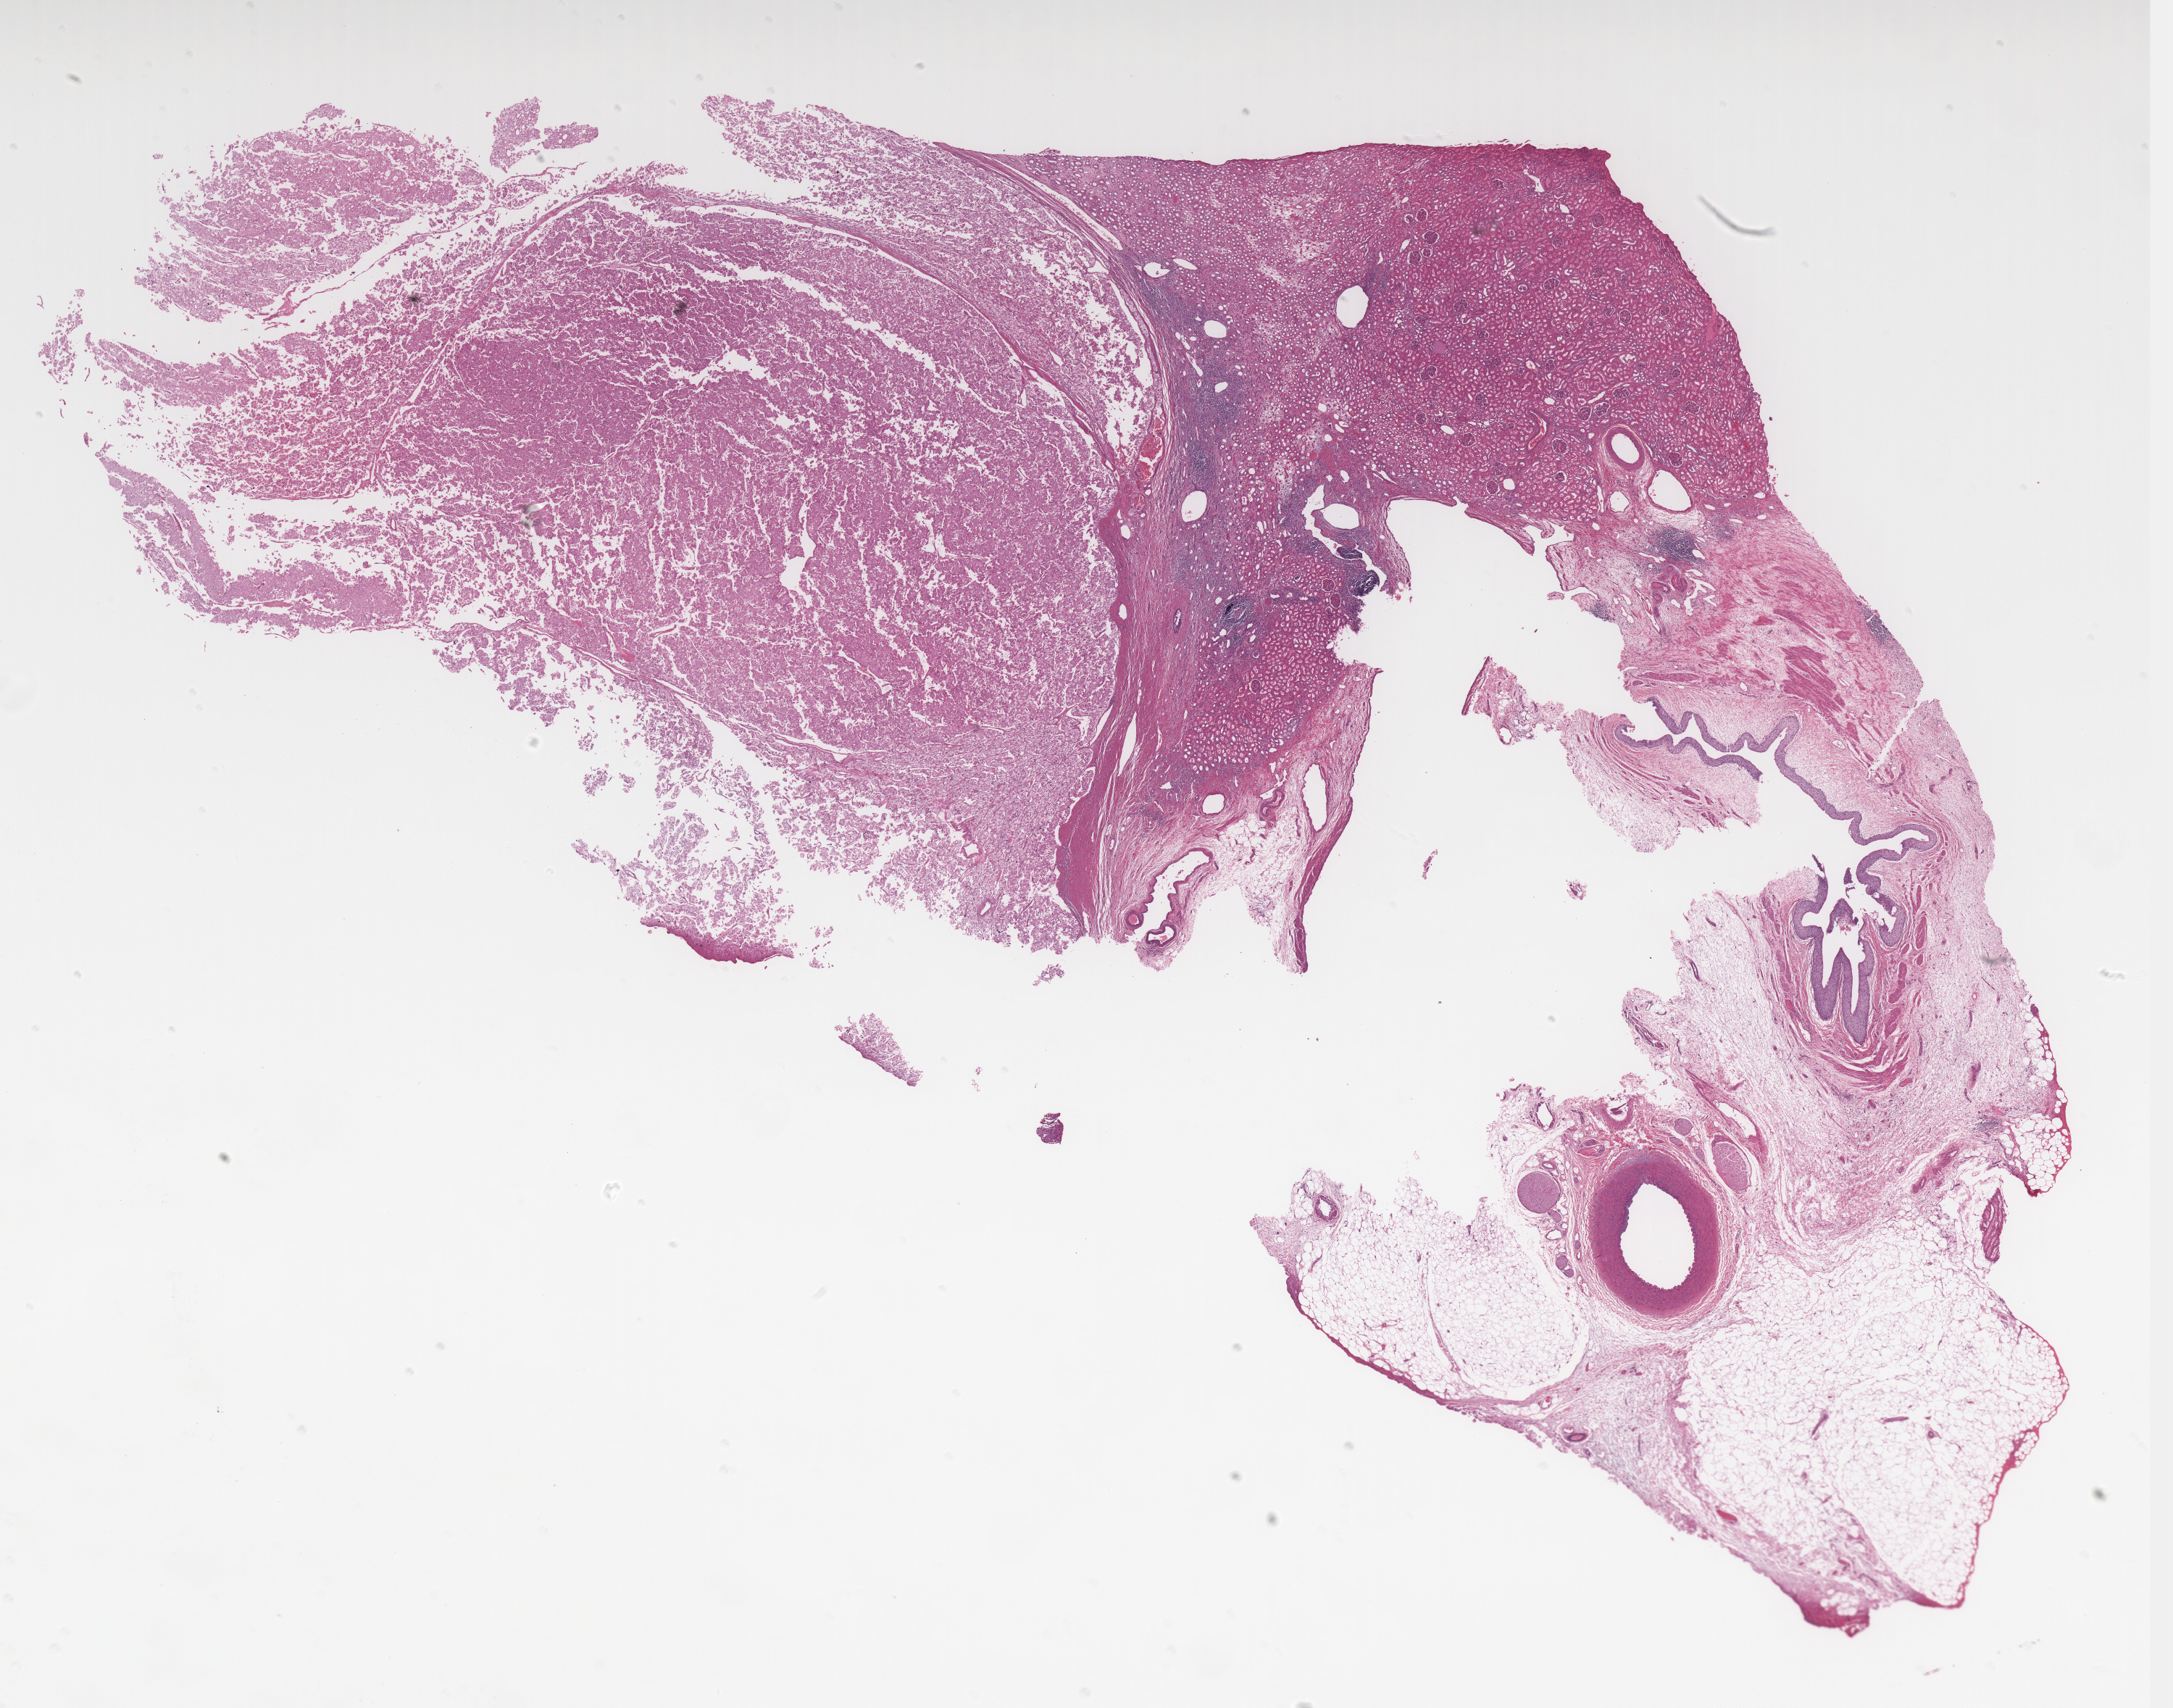
Digitized H&E tissue section (whole slide), a low-resolution overview of the entire scanned area, about 24.0 x 18.8 mm. Formalin-fixed paraffin-embedded (FFPE) diagnostic section. Kidney, primary tumour sample. Patient: male, age at initial diagnosis 26 years.
• lymph nodes positive (case pathology): 0 of 1 examined
• pathologic diagnosis: Renal cell carcinoma, chromophobe type
• AJCC pathologic stage: II (6th edition)